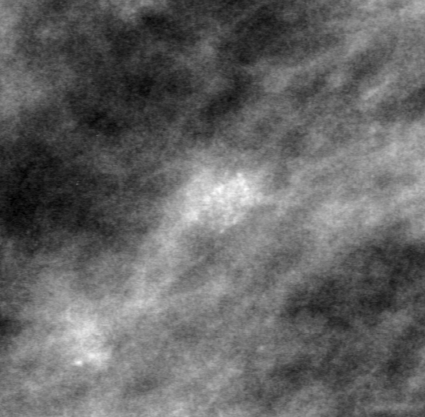
Region of interest cut from a scanned film mammogram (one marked finding); left breast; MLO view.
Finding: calcifications, morphology pleomorphic, distribution clustered; BI-RADS assessment category 4; pathology (as recorded): malignant.